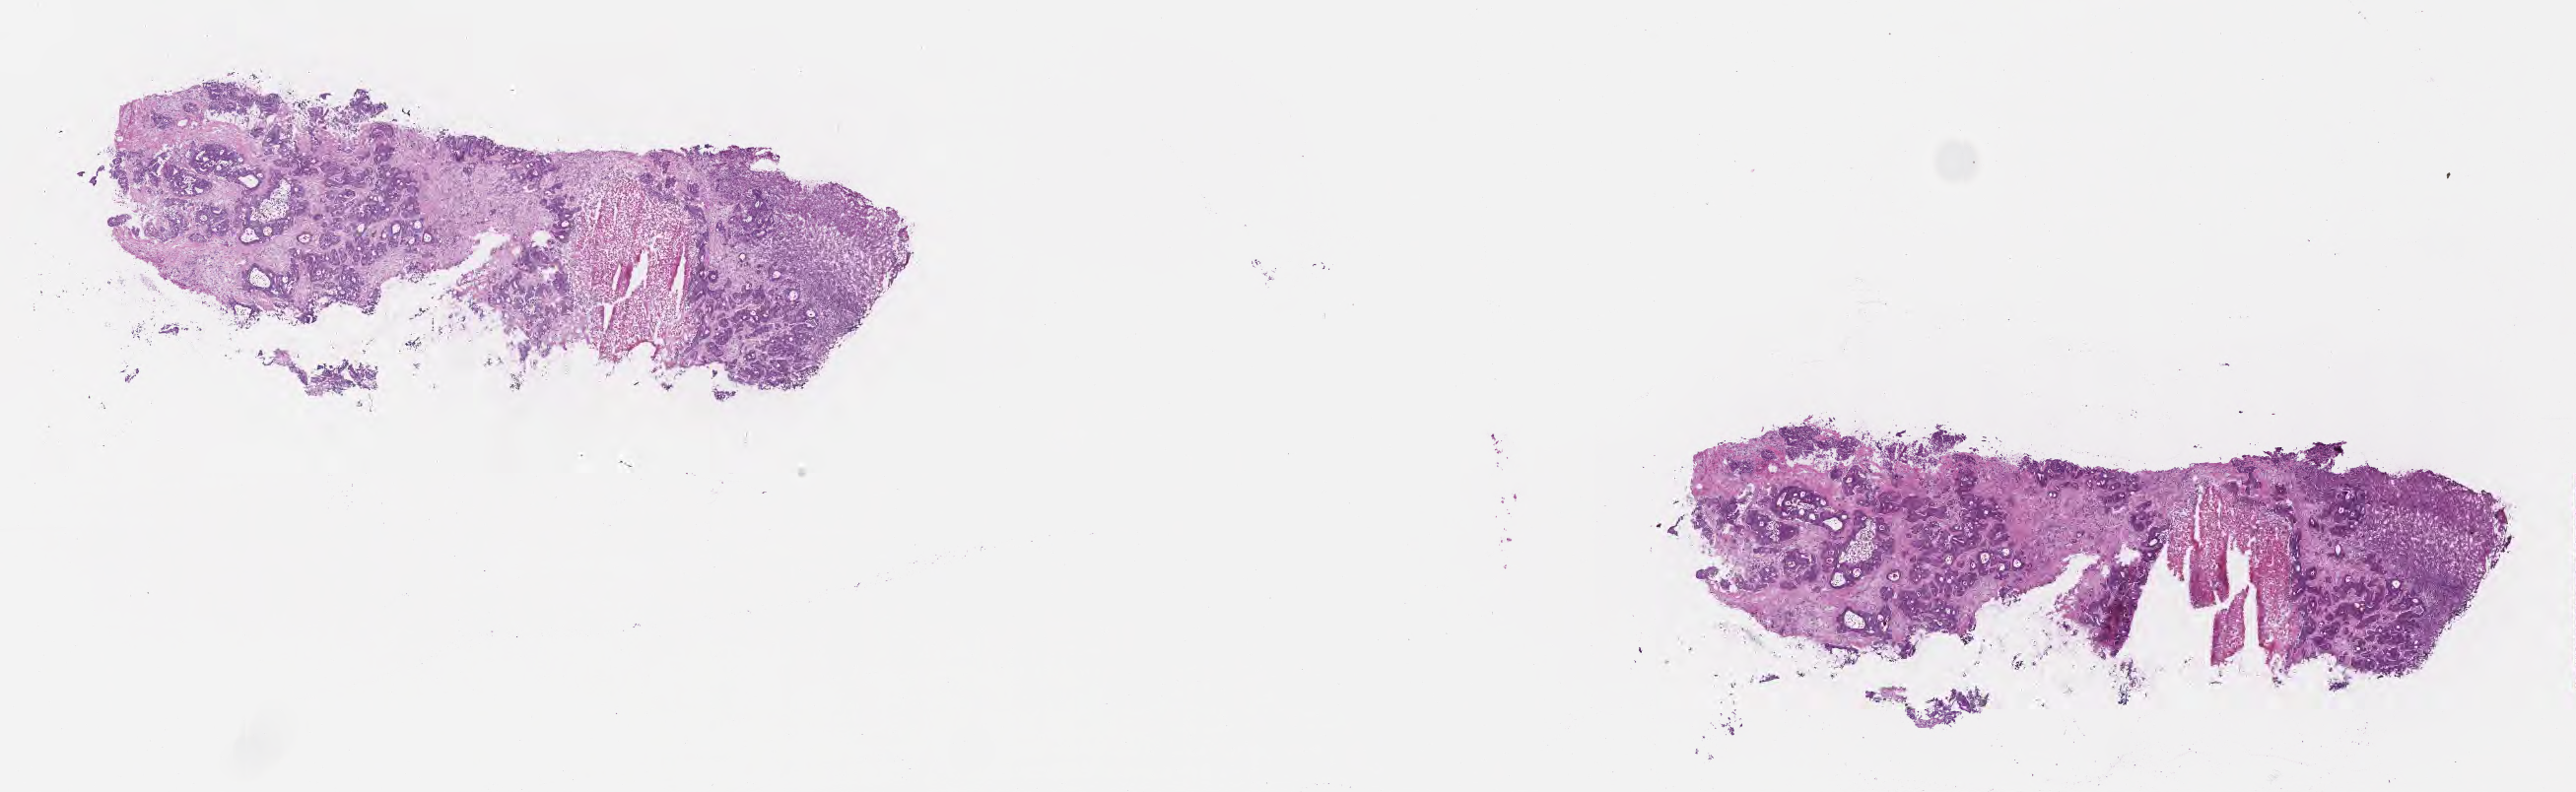
Hematoxylin and eosin (H&E) whole-slide image, shown as a low-resolution overview of the whole scanned area (about 21.1 x 6.5 mm), cryosection, metastatic tumor tissue, resected from liver. Male patient; age at initial diagnosis 63 years. Pathologist review of this section (percent, as recorded): tumor cells 36%, tumor nuclei 73%, stromal cells 34%, necrosis 18%, normal cells 12%. Inflammatory infiltration, as recorded: lymphocyte infiltration 16%, monocyte infiltration 1%, neutrophil infiltration 0%.
Section: top of the tissue portion. Patient diagnosis (primary): Adenocarcinoma, NOS.